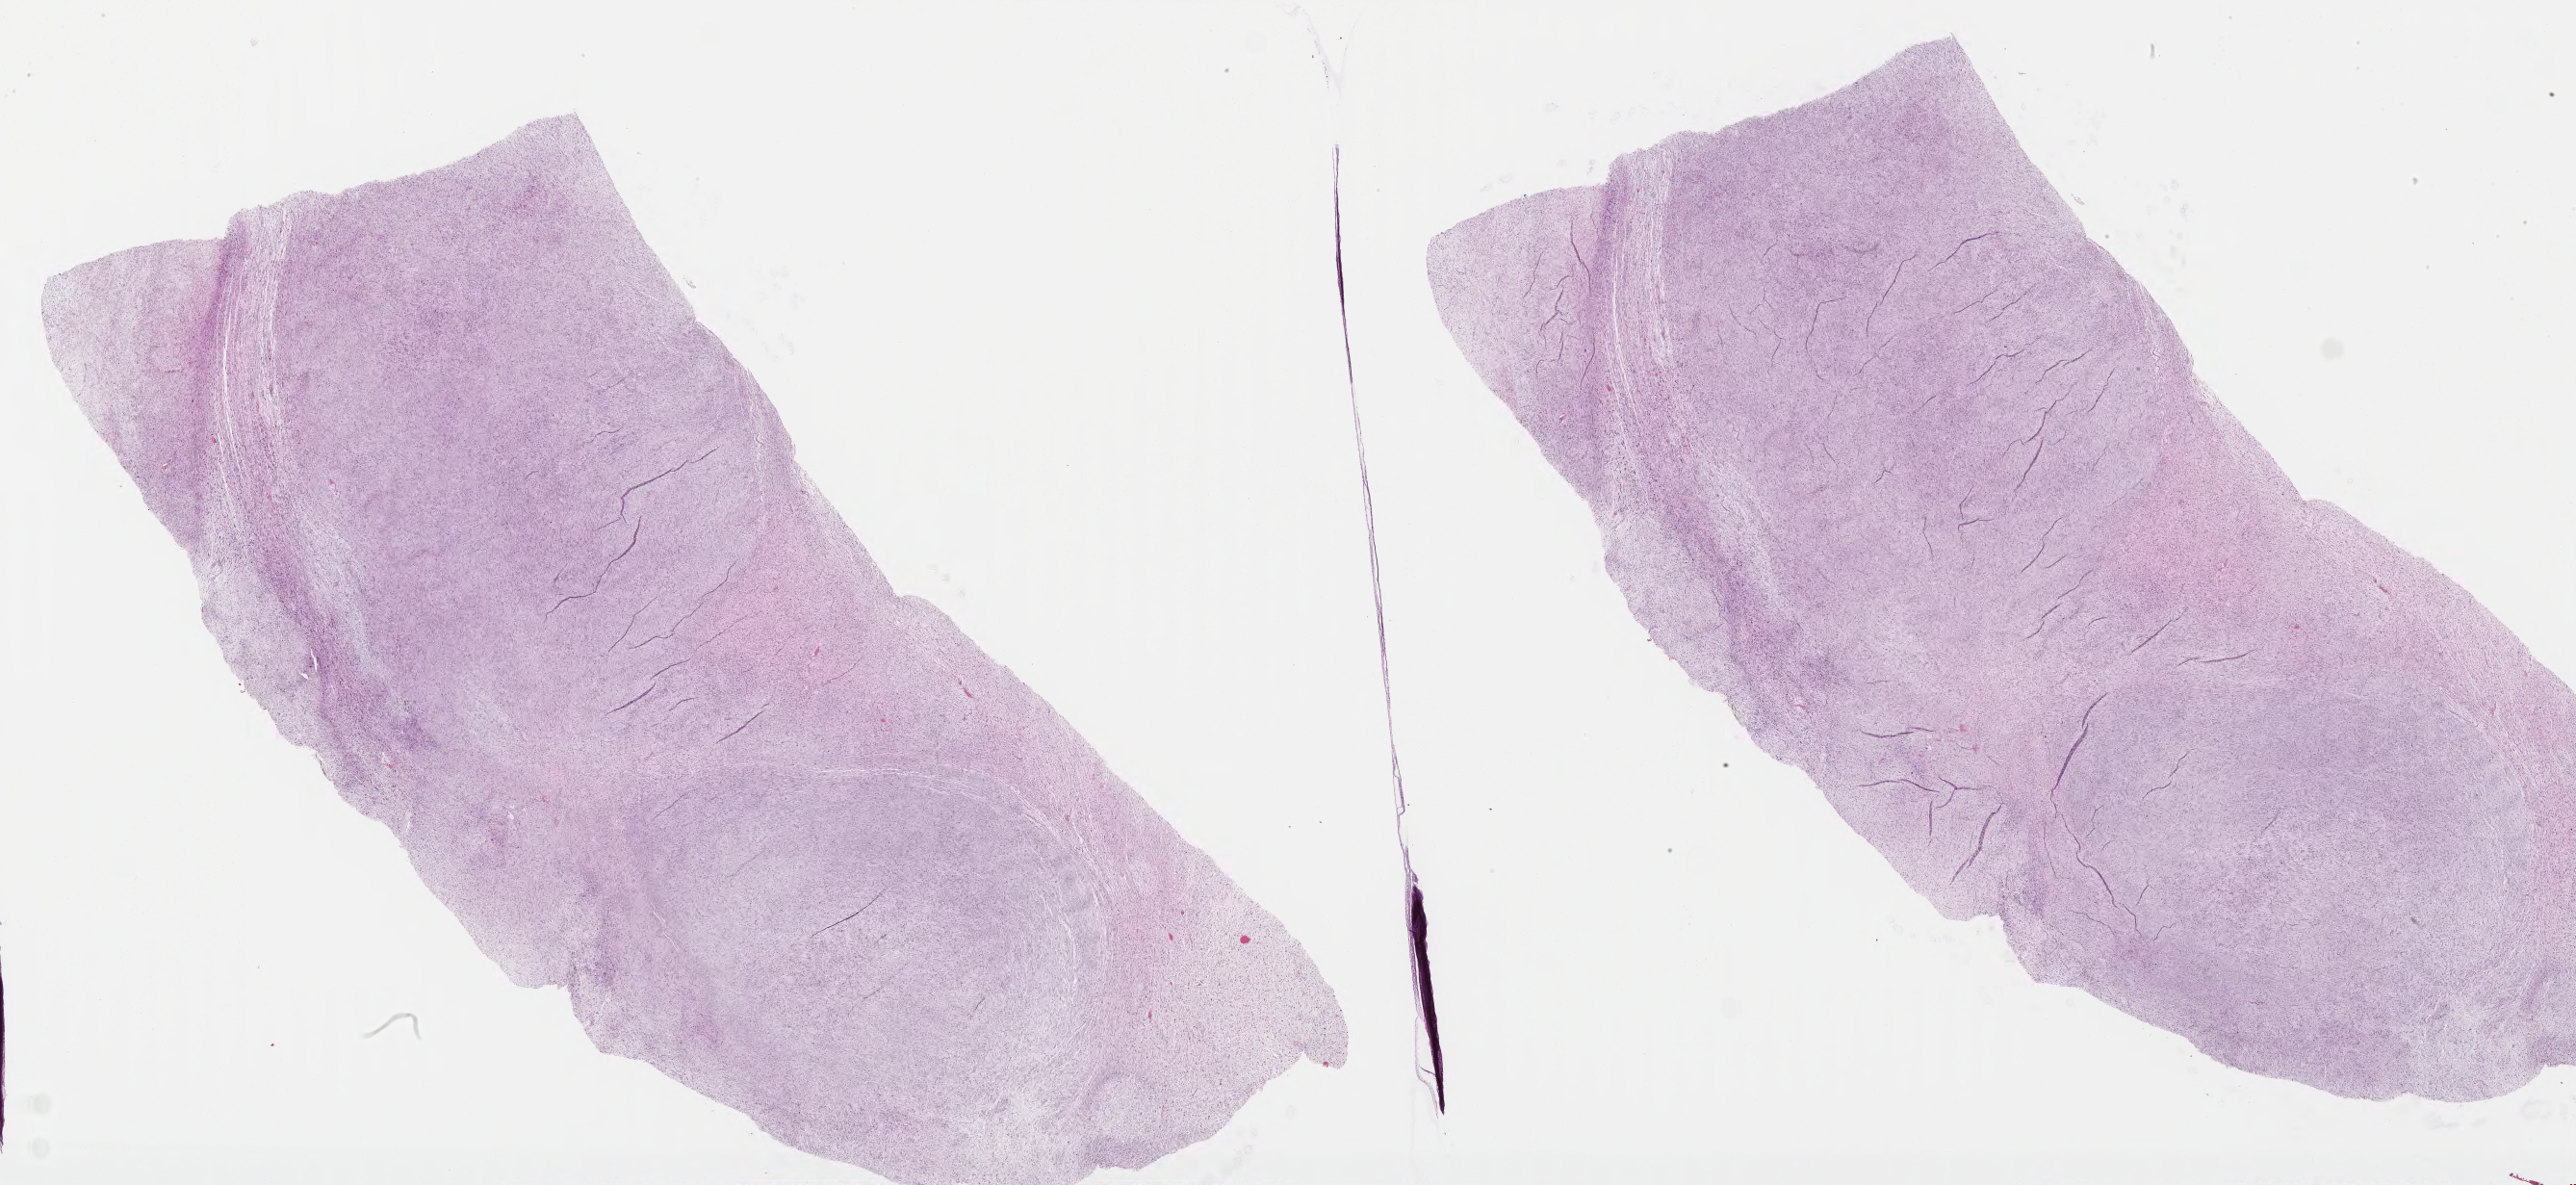
H&E-stained whole-slide image, shown as a low-resolution overview of the whole scanned area (about 43.0 x 19.8 mm, acquisition: 40x scan); formalin-fixed paraffin-embedded (FFPE) diagnostic section; primary tumour sample from the connective, subcutaneous and other soft tissues. Patient: male, age at initial diagnosis 75 years.
Diagnosis: Fibromyxosarcoma (connective, subcutaneous and other soft tissues of thorax).